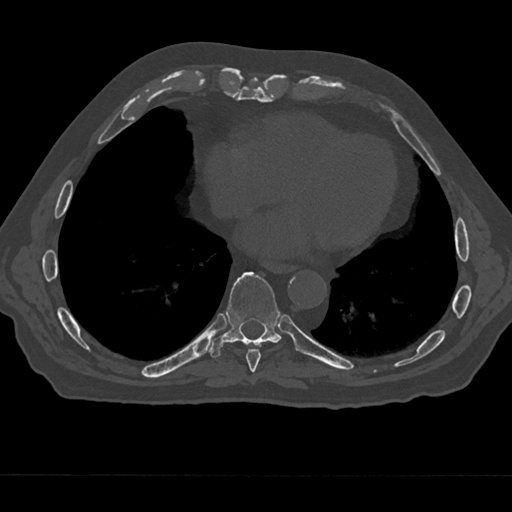
CT including the spine, one axial slice. Slice 282 of 797 in the series (ordered by position). Reconstruction kernel Br40s/3. 120 kVp. Bone window (W 1800 / L 400 HU). 512 × 512 image matrix, field of view 377 × 377 mm. Patient: male, 75 years. From the clinical record (not read from this slice): primary cancer: renal; vertebrae with lytic lesions (as recorded): T4.
Annotated regions visible in this slice (semi-automatic segmentation, software-assisted and operator-edited):
- T8 vertebra: box from (x=246, y=349) to (x=261, y=372) px
- T9 vertebra: (x=209, y=272)–(x=296, y=357)